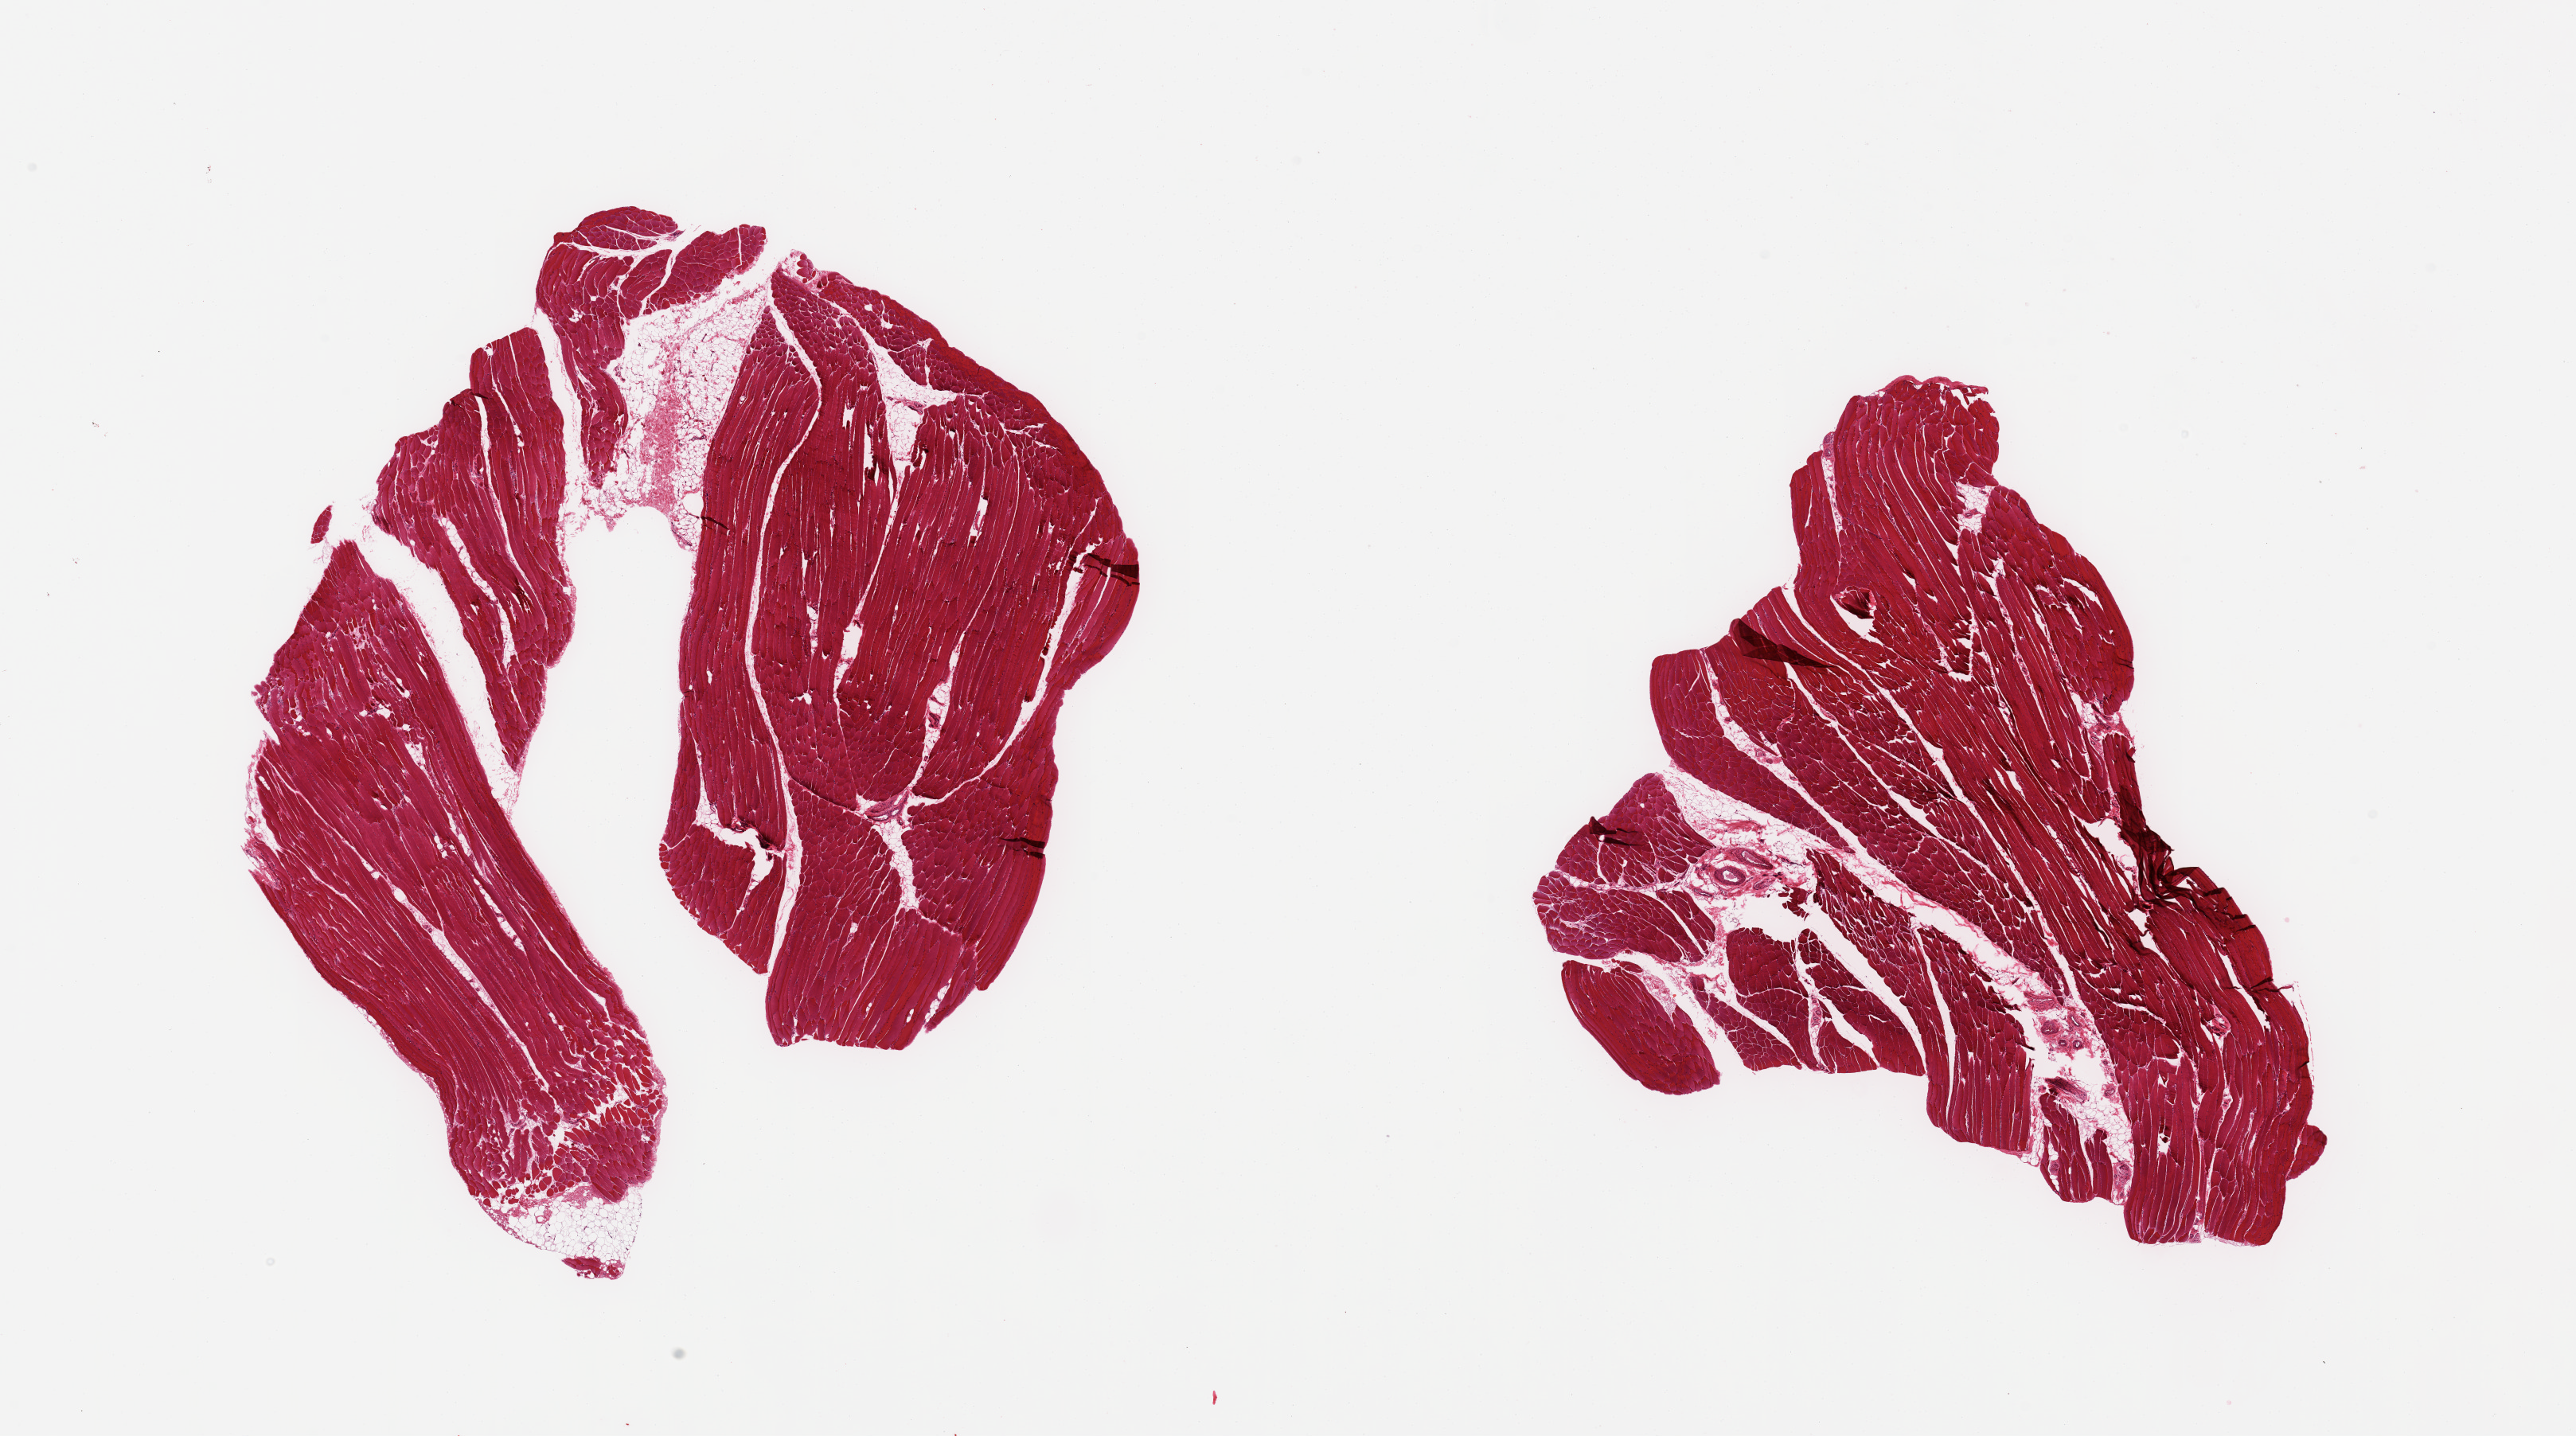
Digitized haematoxylin and eosin-stained section — whole scanned area (about 25.6 x 14.3 mm, slide scanned at 20x) shown as a low-resolution overview, PAXgene-fixed, paraffin-embedded tissue, sampled site (target tissue): skeletal muscle, donor tissue sample. Donor sex: male.
Pathologist's review note for this sample: 2 pieces, interstitial fat/vascular elements are ~10% of tissue.